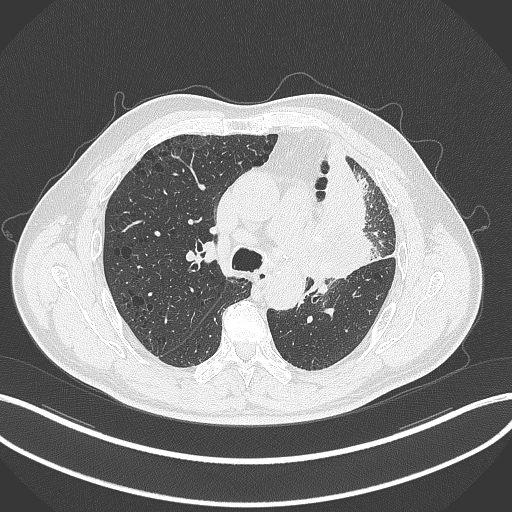
Chest CT, one axial slice. Slice 199 of 297 in the series (ordered by position). Lung window (W 1500 / L -600 HU). 1 mm slice thickness. 512 × 512 image matrix. Male patient, age 68 years. Case-level facts recorded for this patient, not image findings: clinical TNM (as recorded): T3 N3 M1.
Annotated regions visible in this slice (bounding box drawn by a radiologist):
- lung tumour (recorded histology: adenocarcinoma): bounding box <304,143,396,289> (left, top, right, bottom; pixels)